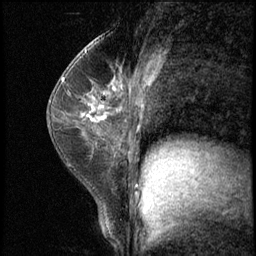
Breast MRI (dynamic contrast-enhanced), one sagittal slice. Position 36 of 62 along the scan axis. 3 images stored at this slice position (order not interpretable as contrast timing). 1.5 T. TE 4.2 ms, TR 8.7 ms. 2.5 mm slice thickness. 256 × 256 image matrix, field of view 180 × 180 mm. Female patient, age 35 years. Case-level facts recorded for this patient, not image findings: setting: breast cancer imaged before/during neoadjuvant chemotherapy; receptor status: HER2-positive.
Outlined on this slice (semi-automatically segmented with operator editing):
- analysis volume of interest (the breast-tissue region the enhancement analysis was run in; not a lesion): bounding box (x1, y1, x2, y2) in pixels: (71, 78, 120, 139)
- tumour enhancement mask (voxels above the 140 % enhancement threshold inside the analysis volume of interest): (83, 100, 106, 120)